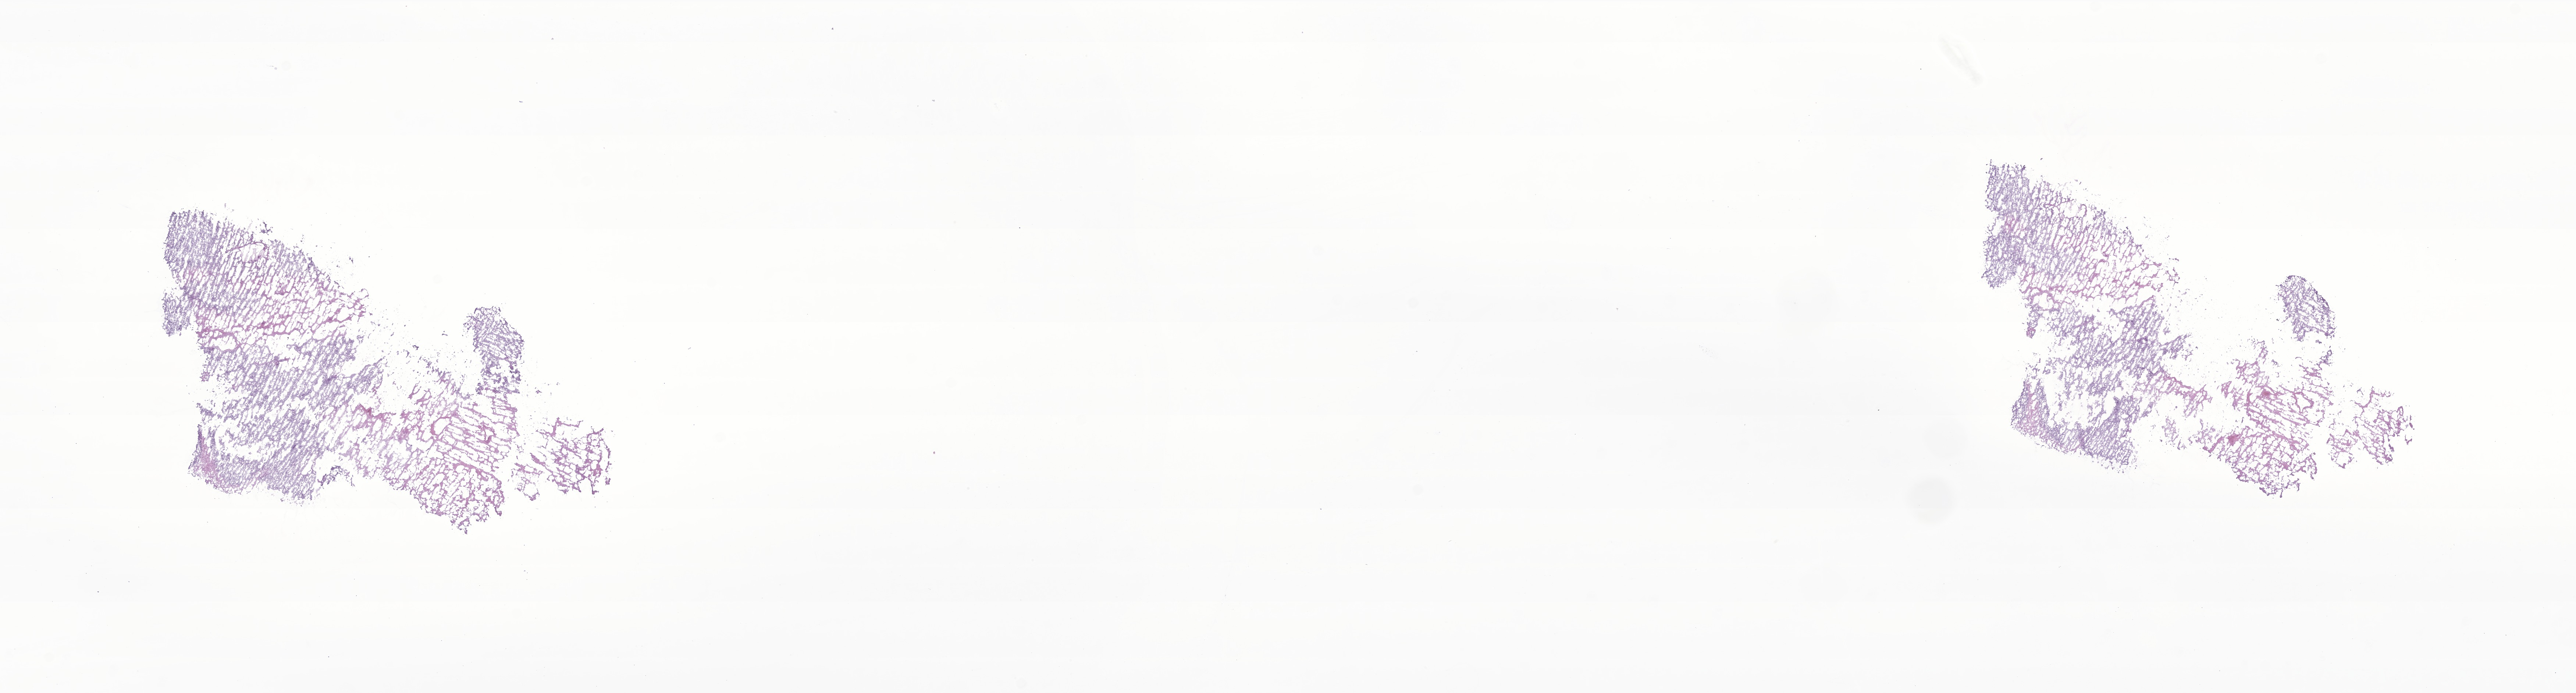
Digitized hematoxylin and eosin (H&E)-stained section of tumor tissue from the soft tissue of thorax, low-resolution overview of the scanned area, about 29.5 x 7.9 mm; cryosection (OCT / tissue freezing medium). Patient female; age 197 months (16 years 5 months).
- diagnosis (ICD-O-3 morphology term): Undifferentiated sarcoma
- tissue or organ of origin (case record): connective, subcutaneous and other soft tissues of thorax